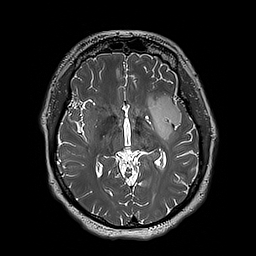
Brain MRI from a brain-tumour surgery series, one axial slice. 1 mm slice thickness. 256 × 256 image matrix, field of view 250 × 250 mm. From the clinical record (not read from this slice): histopathology: Astrocytoma; WHO grade: 3; IDH mutation: yes; tumour location: Left Insular.
Structures marked on this image (outlined manually by an expert reader):
- tumour: bounding box [x1, y1, x2, y2] px = [148, 95, 181, 142]